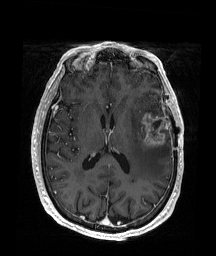
Brain MRI from a brain-tumour surgery series, one axial slice. Slice 87 of 176 in the series (ordered by position). T1-weighted post-contrast. 1 mm slice thickness. 216 × 256 image matrix, field of view 219 × 260 mm. Case-level facts recorded for this patient, not image findings: histopathology: Glioblastoma; WHO grade: 4; IDH mutation: no; tumour location: Left Frontal.
Structures marked on this image (expert manual segmentation):
- tumour: box from (x=138, y=113) to (x=168, y=149) px